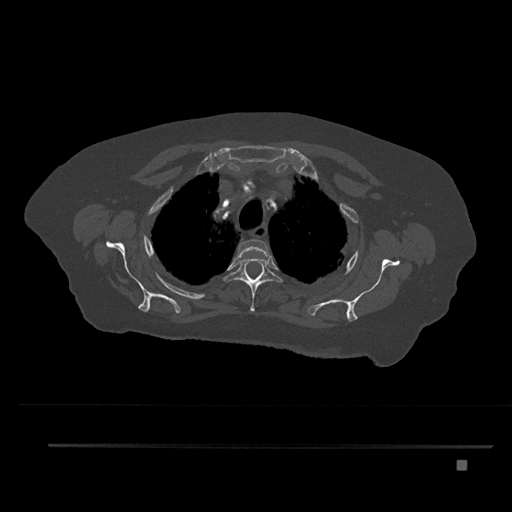
CT including the spine, one axial slice. Slice 643 of 797 in the series (ordered by position). 120 kVp. Bone window (W 1800 / L 400 HU). 512 × 512 image matrix, field of view 437 × 437 mm. Female patient, age 76 years. Case-level facts recorded for this patient, not image findings: primary cancer: lung.
Structures marked on this image (semi-automatic segmentation, software-assisted and operator-edited):
- T2 vertebra: bounding box [x1, y1, x2, y2] px = [237, 239, 270, 258]
- T3 vertebra: [223, 257, 283, 312]